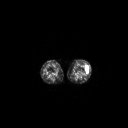
FDG PET of an extremity soft-tissue mass (from a PET/CT study), one axial slice. Slice 167 of 223 in the series (ordered by position). 3.27 mm slice thickness. 128 × 128 image matrix. Patient: female, 16 years. From the clinical record (not read from this slice): histological type: spindle cell suggestive of biphasic synovial sarcoma; grade: intermediate; site of the primary tumour: left knee.
Outlined on this slice (expert contour drawn on MRI and transferred to this co-registered scan by the dataset authors):
- gross tumour volume including surrounding oedema: box from (x=85, y=66) to (x=88, y=73) px
- gross tumour volume (mass): (x=85, y=67)–(x=88, y=73)